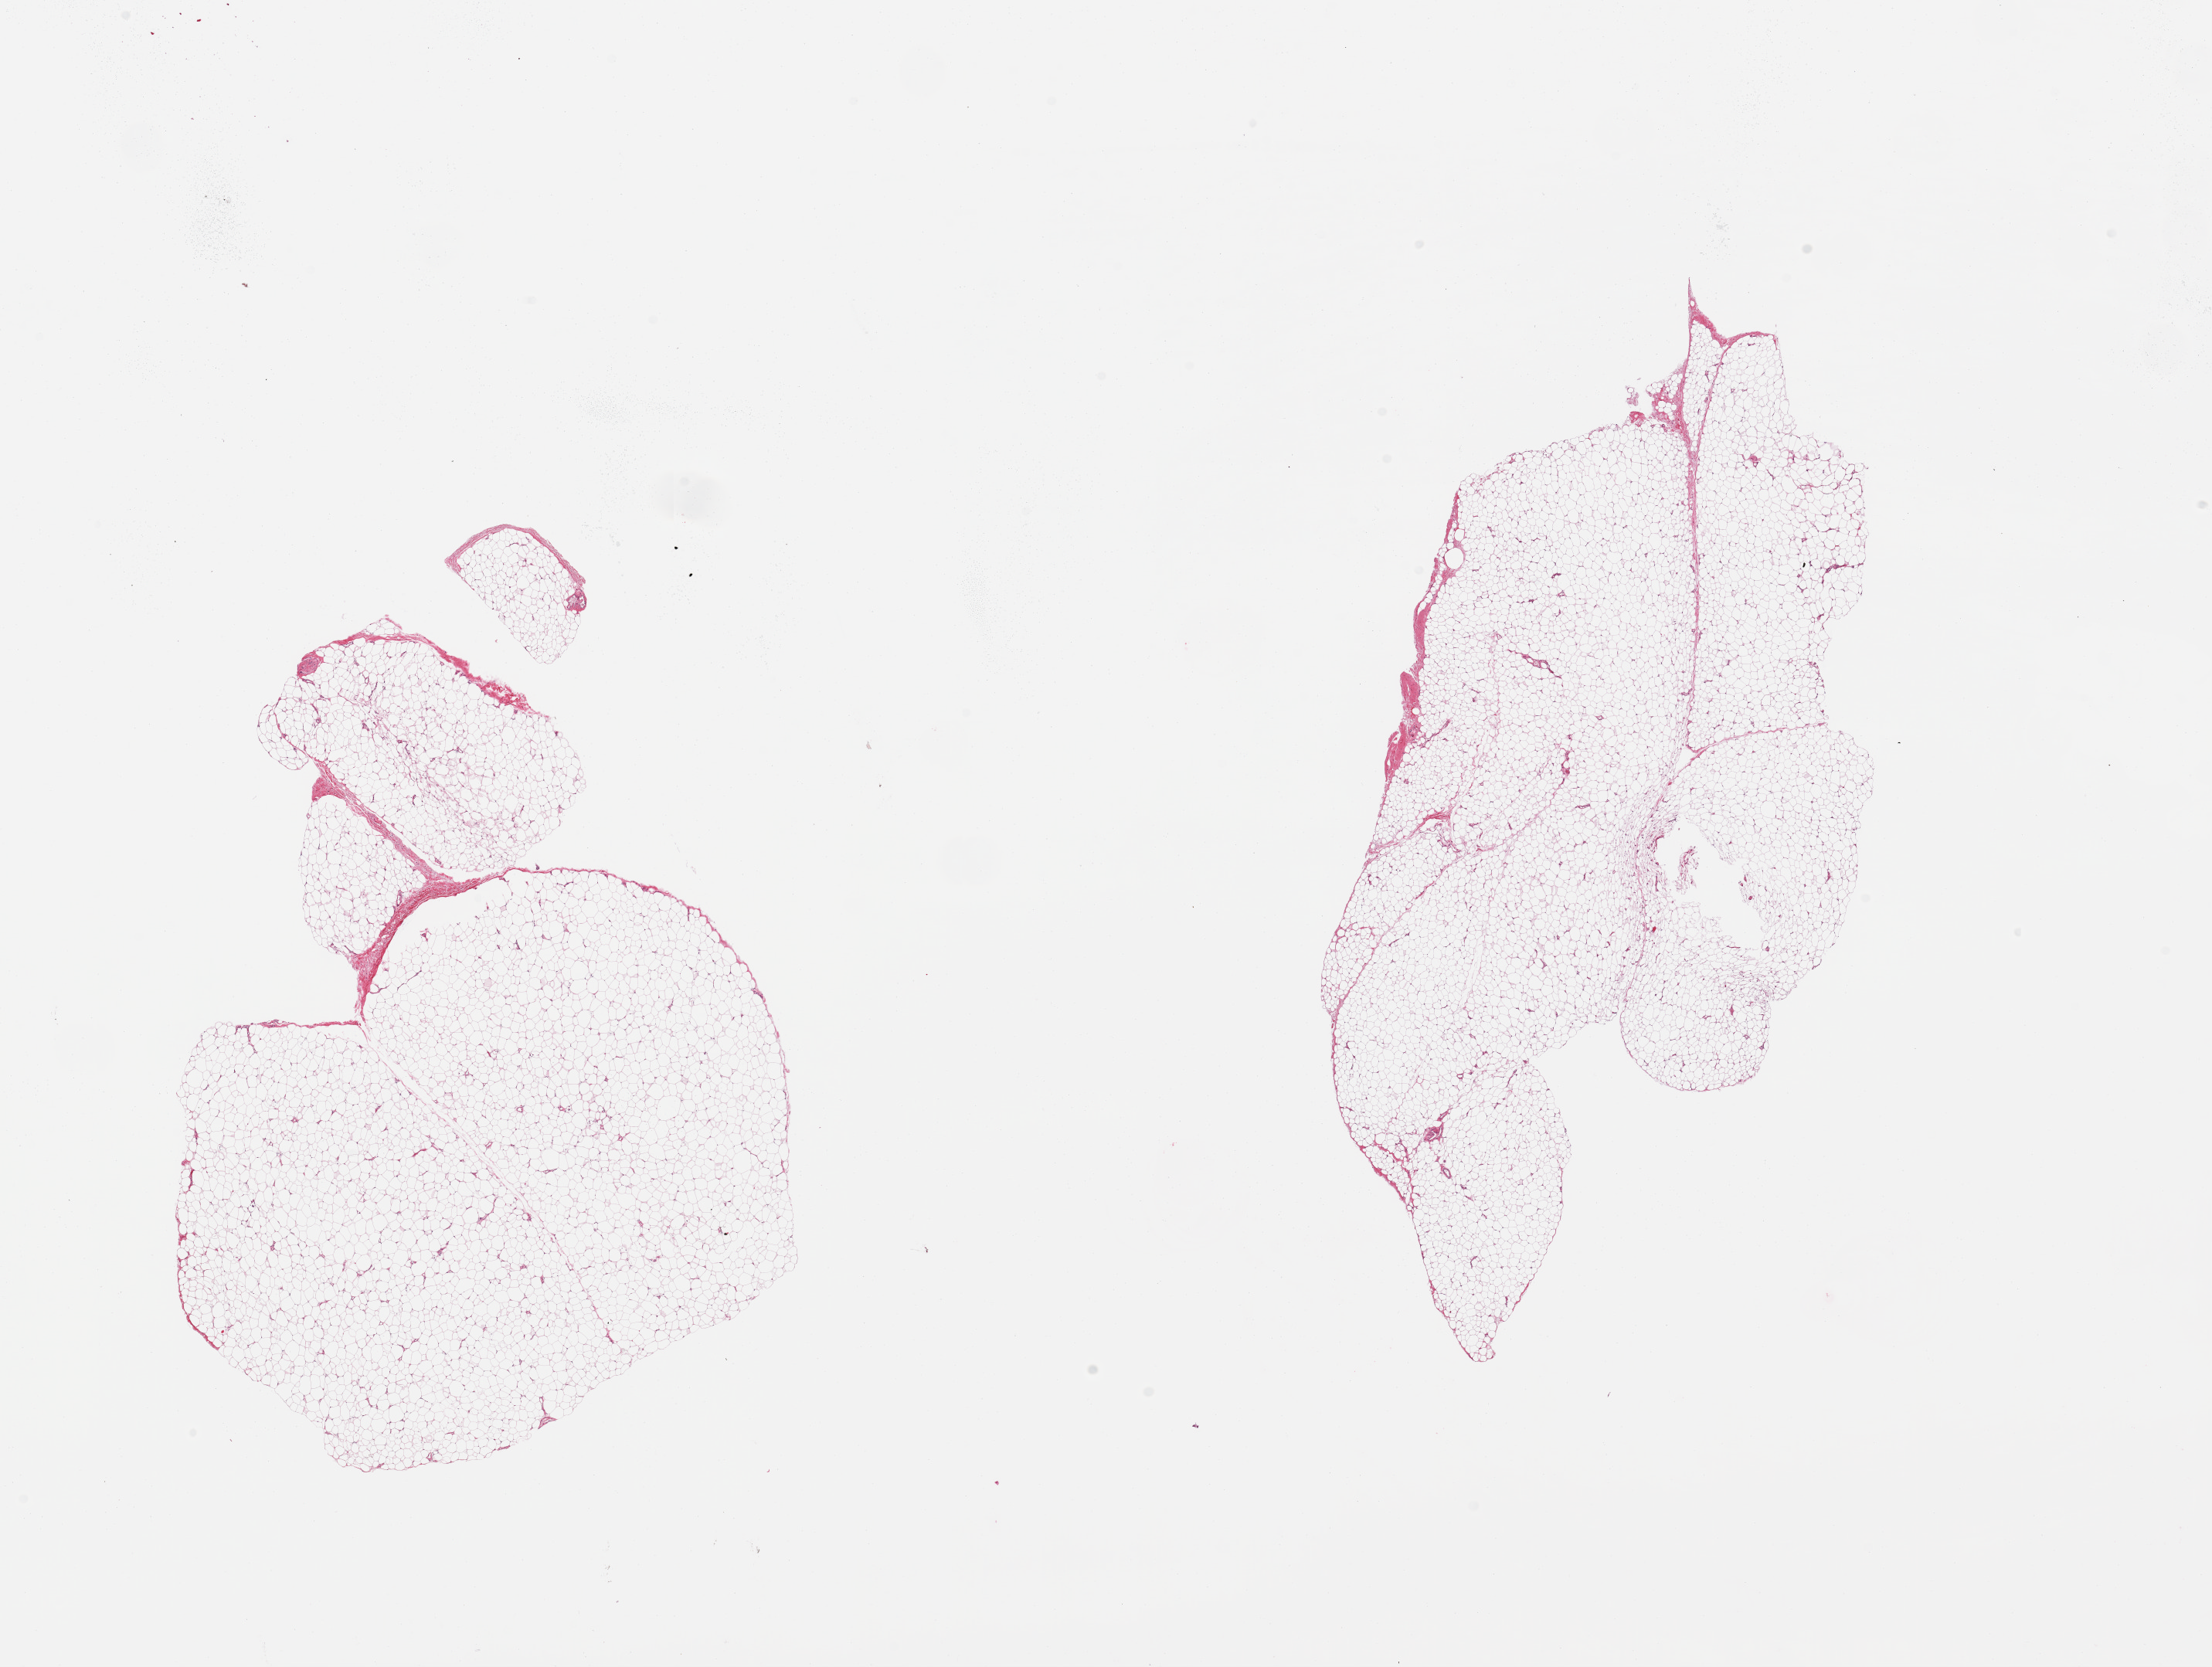
Digitized haematoxylin and eosin-stained section, whole scanned area (about 22.6 x 17.1 mm, from a 20x scan) shown as a low-resolution overview, PAXgene-fixed, paraffin-embedded tissue, target tissue: adipose tissue, donor tissue sample. Donor: female.
- pathologist's review note for this sample: 2 pieces; mature fat